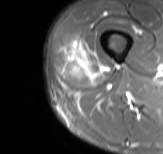
MRI of an extremity soft-tissue mass, one axial slice; slice 18 of 61 in the series (ordered by position); STIR; MR volume resampled by the dataset authors to the PET/CT grid (not the native acquisition matrix); 163 × 154 image matrix, field of view 159 × 150 mm. Male patient. Case-level facts recorded for this patient, not image findings: histological type: poorly differentiated synovial sarcoma; grade: high; site of the primary tumour: right buttock.
Outlined on this slice (expert contour drawn on MRI and transferred to this co-registered scan by the dataset authors):
- gross tumour volume including surrounding oedema: box from (x=64, y=39) to (x=106, y=81) px